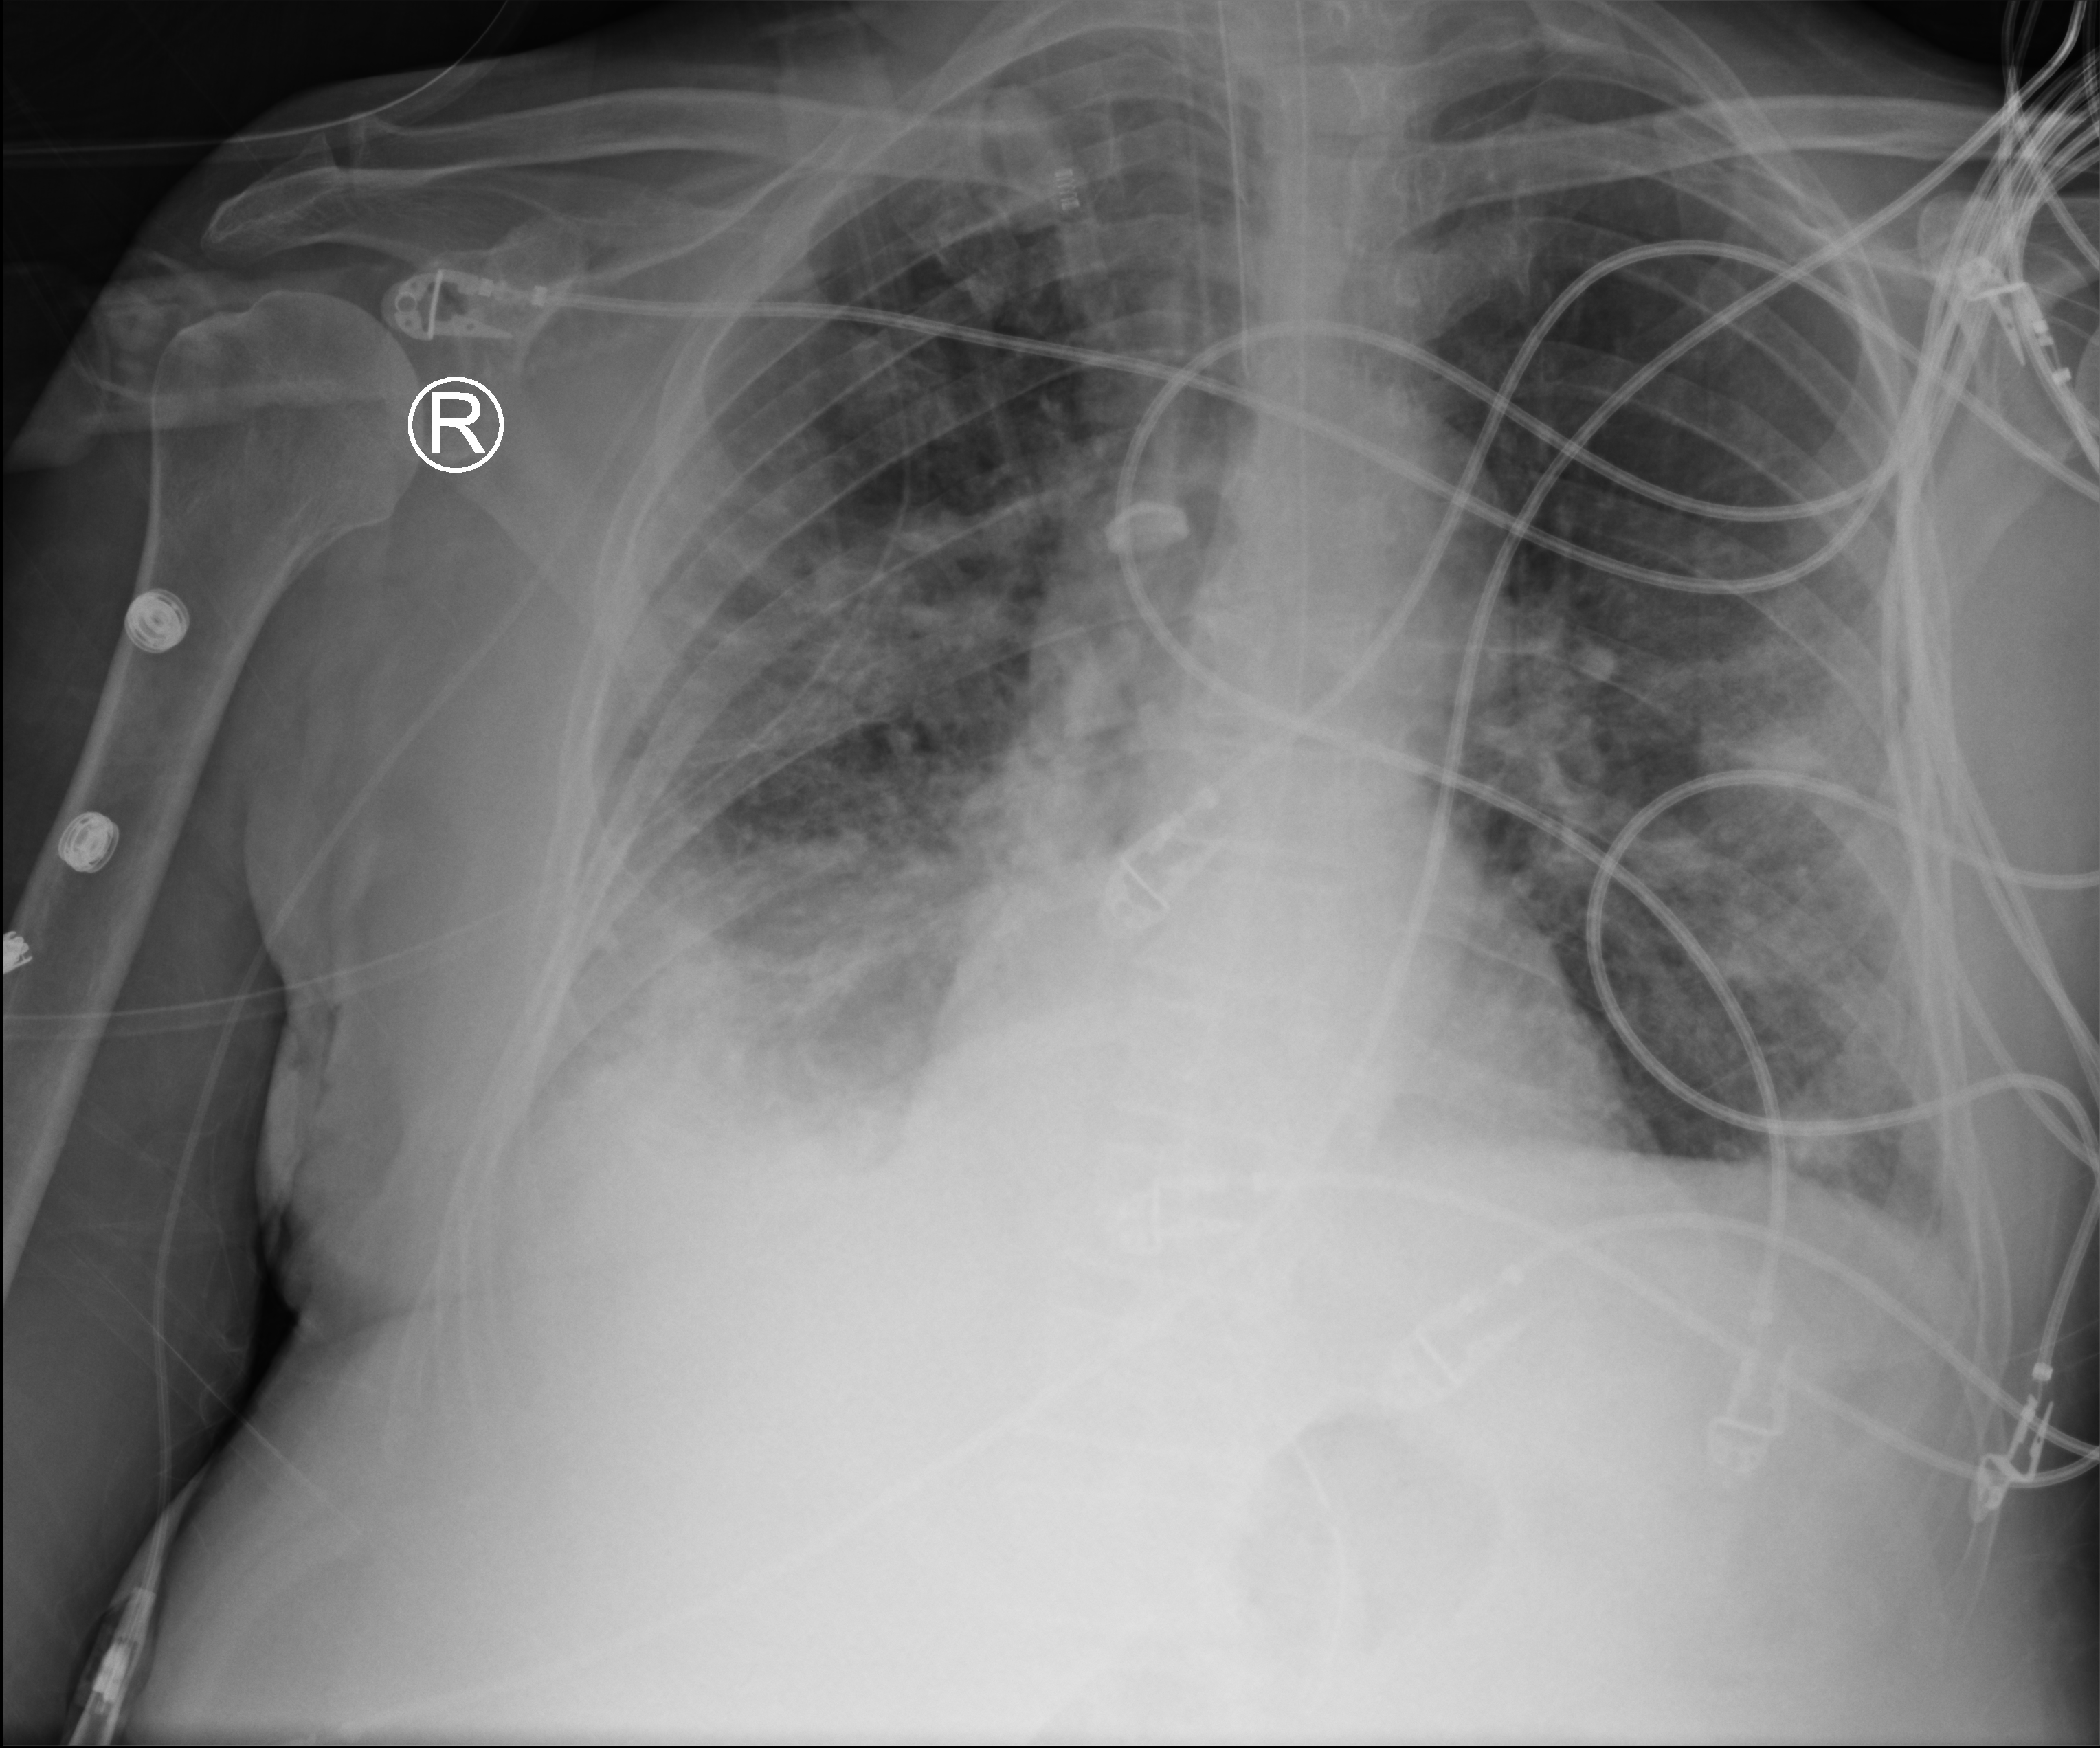
Chest X-ray (portable). Male patient hospitalised with COVID-19, age 75–90 years.
Hospital-stay facts (about this admission, not read from this image; timing relative to this image not recorded): mechanically ventilated during this hospital stay: yes.